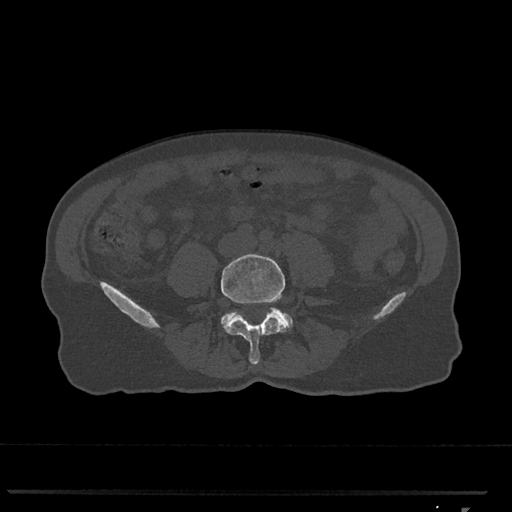
CT including the spine, one axial slice; position 192 of 793 along the scan axis; 120 kVp; bone window (W 1800 / L 400 HU); 0.5 mm slice thickness; 512 × 512 image matrix, field of view 380 × 380 mm. Patient: female, 62 years. Case-level facts recorded for this patient, not image findings: primary cancer: renal.
Structures marked on this image (semi-automatic segmentation, software-assisted and operator-edited):
- L4 vertebra: bounding box [x1, y1, x2, y2] px = [221, 254, 288, 365]
- L5 vertebra: [221, 309, 293, 329]